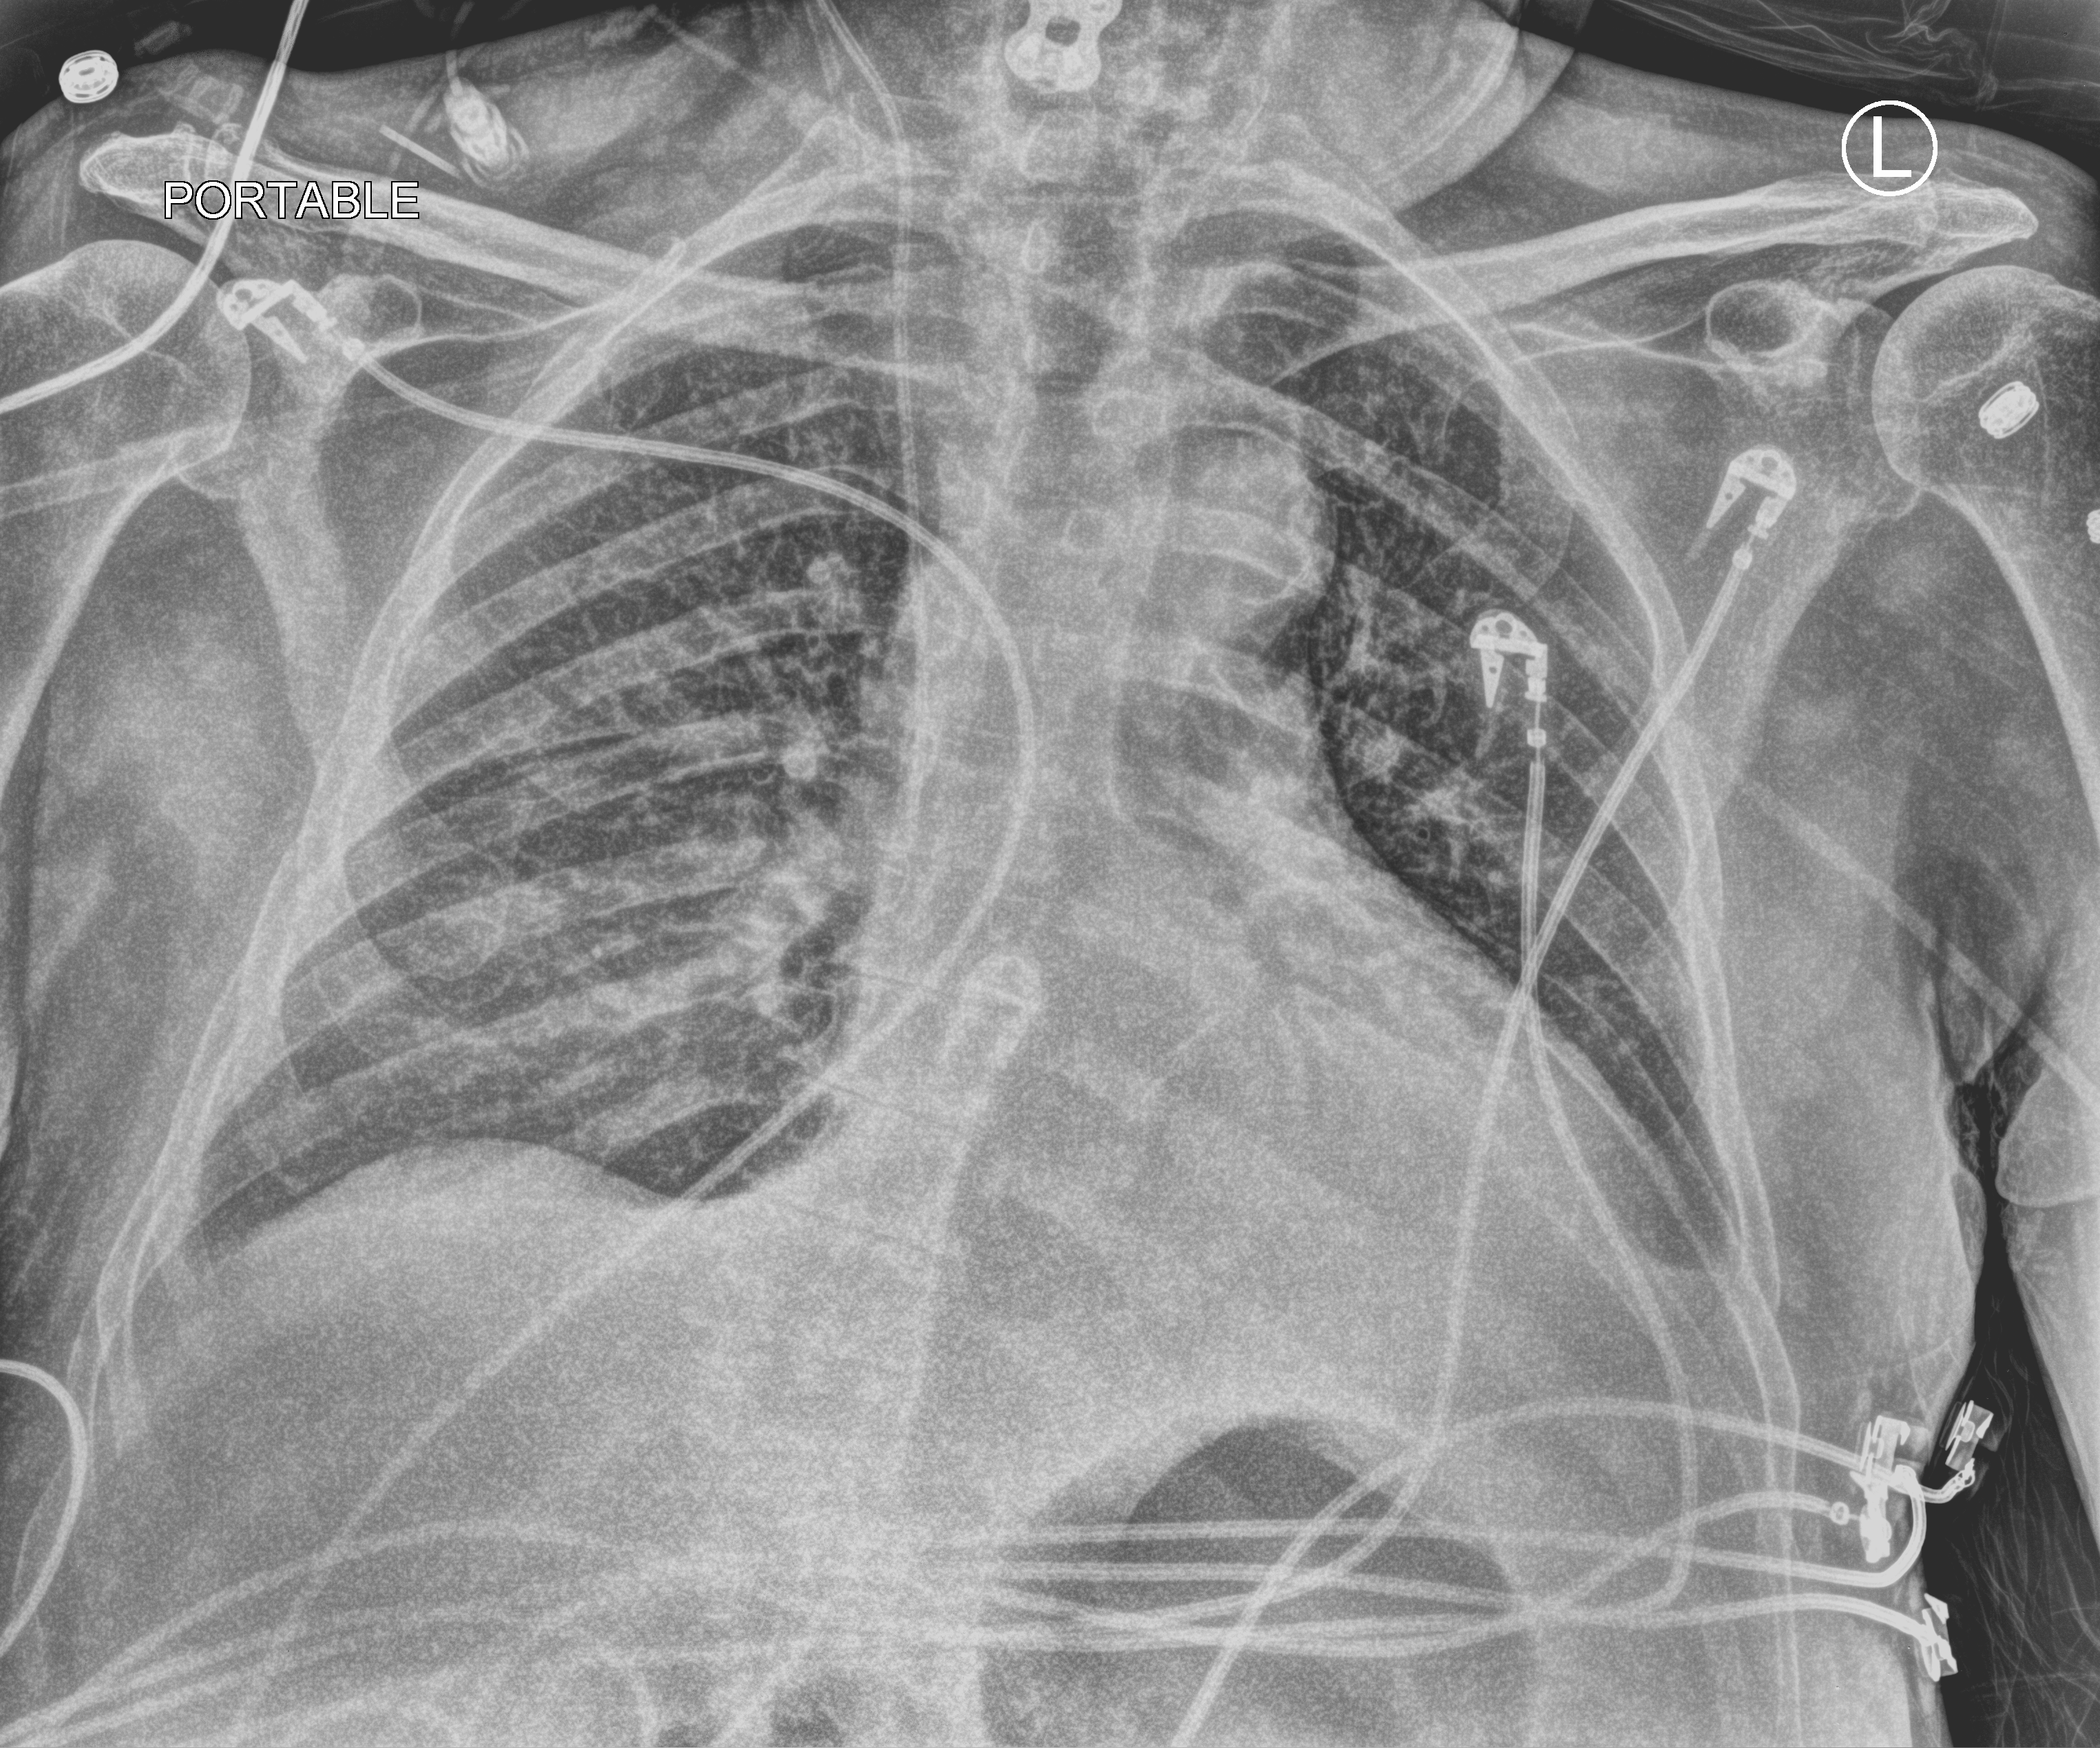
Portable chest radiograph. Patient hospitalised with COVID-19; male, aged 75–90 years.
Hospital-stay facts (about this admission, not read from this image; timing relative to this image not recorded):
- mechanically ventilated during this hospital stay: no
- diabetes (admission record): yes